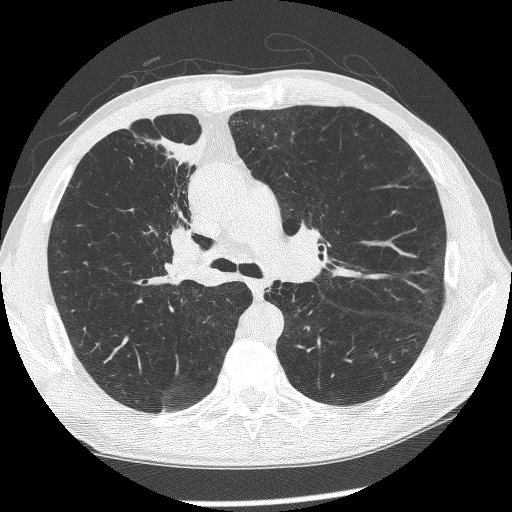
Chest CT (low-dose screening protocol), one axial image. First (baseline) screen. Lung window (W 1500 / L -600 HU). 1.25 mm slice thickness. Male, age 60 years at enrolment.
Expert reader's lesion annotation, bounding box [x1, y1, x2, y2] px = [144, 200, 222, 293]. Reader record for this screening exam (exam-level; its link to the box is not recorded): non-calcified nodule or mass ≥4 mm, right upper lobe, 12 × 8 mm, spiculated (stellate) margins, mixed attenuation. Official screen result: positive, change unspecified: nodule(s) >= 4 mm or enlarging nodule(s), mass(es), or other non-specific abnormalities suspicious for lung cancer. Participant outcome: lung cancer diagnosed 208 days after this screen — squamous cell carcinoma, NOS, right upper lobe, right middle lobe, right main stem bronchus, poorly differentiated (G3), stage IV (AJCC 6th edition).